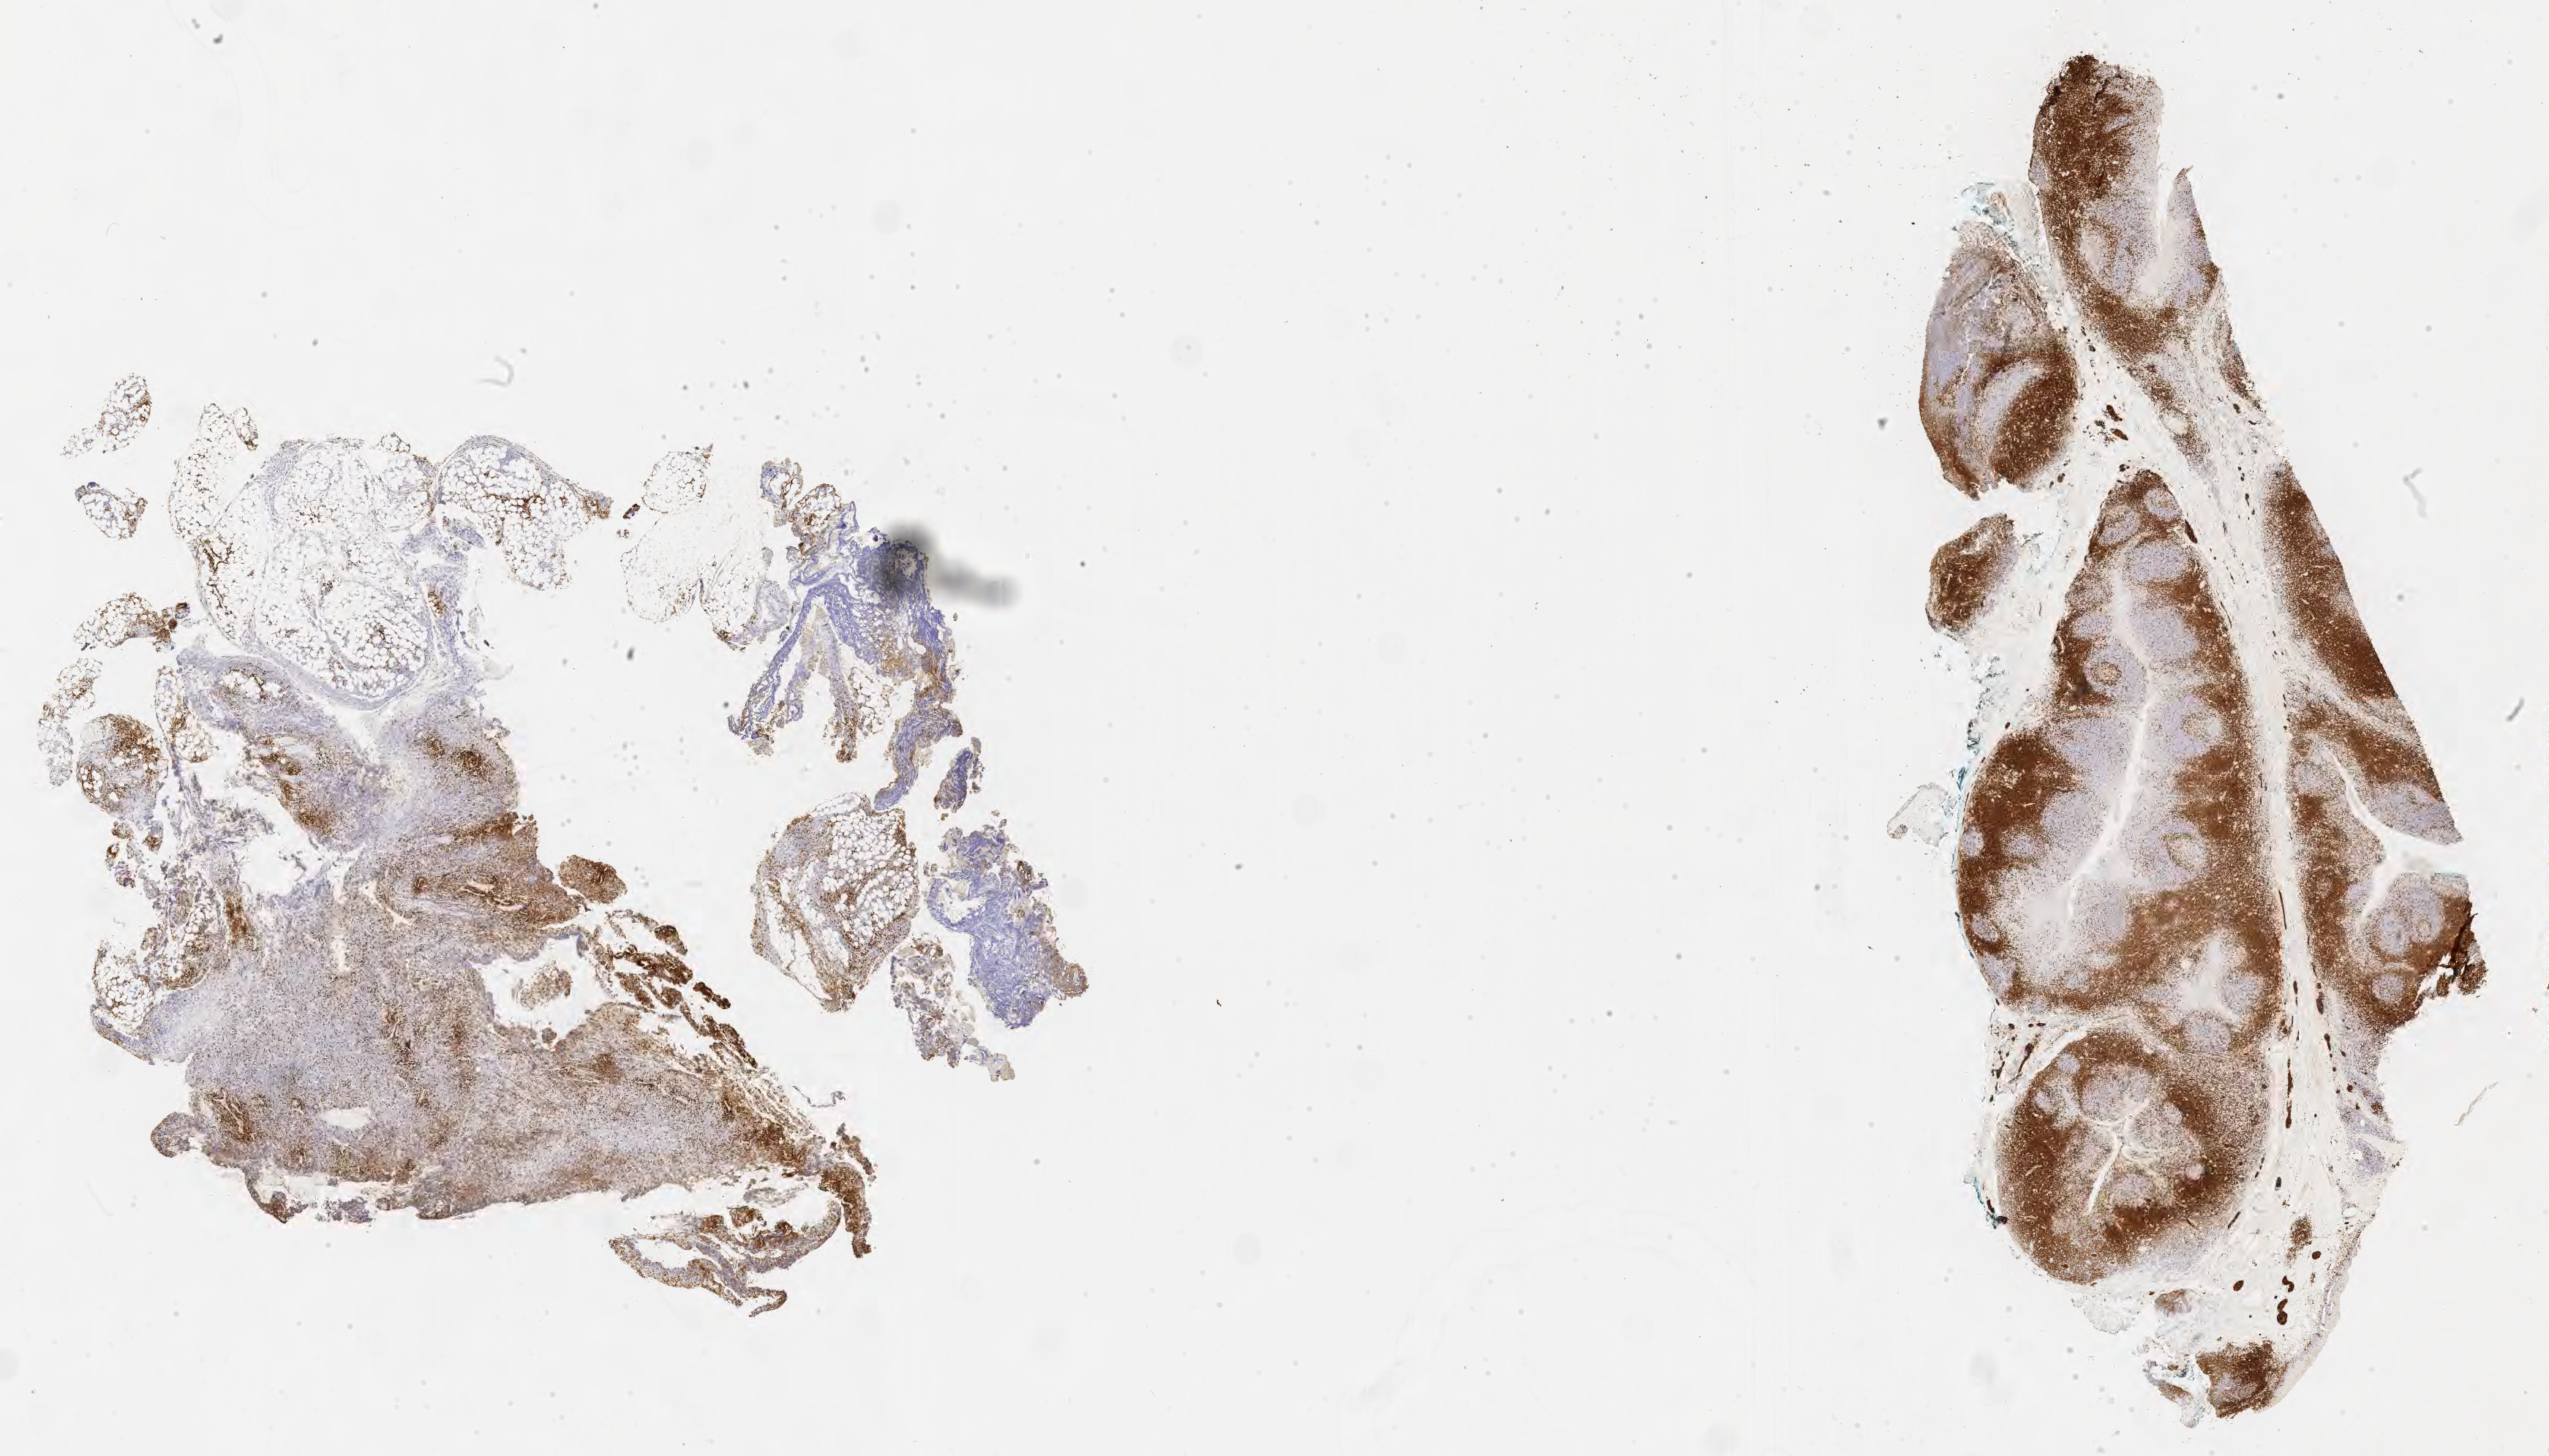
Immunohistochemistry (IHC) whole-slide image stained for CD3 — whole scanned area (about 28.2 x 16.1 mm) shown as a low-resolution overview; tumor tissue; site: abdominal lymph node. Male, age 9 years at initial diagnosis.
Diagnosis: Burkitt lymphoma, NOS.